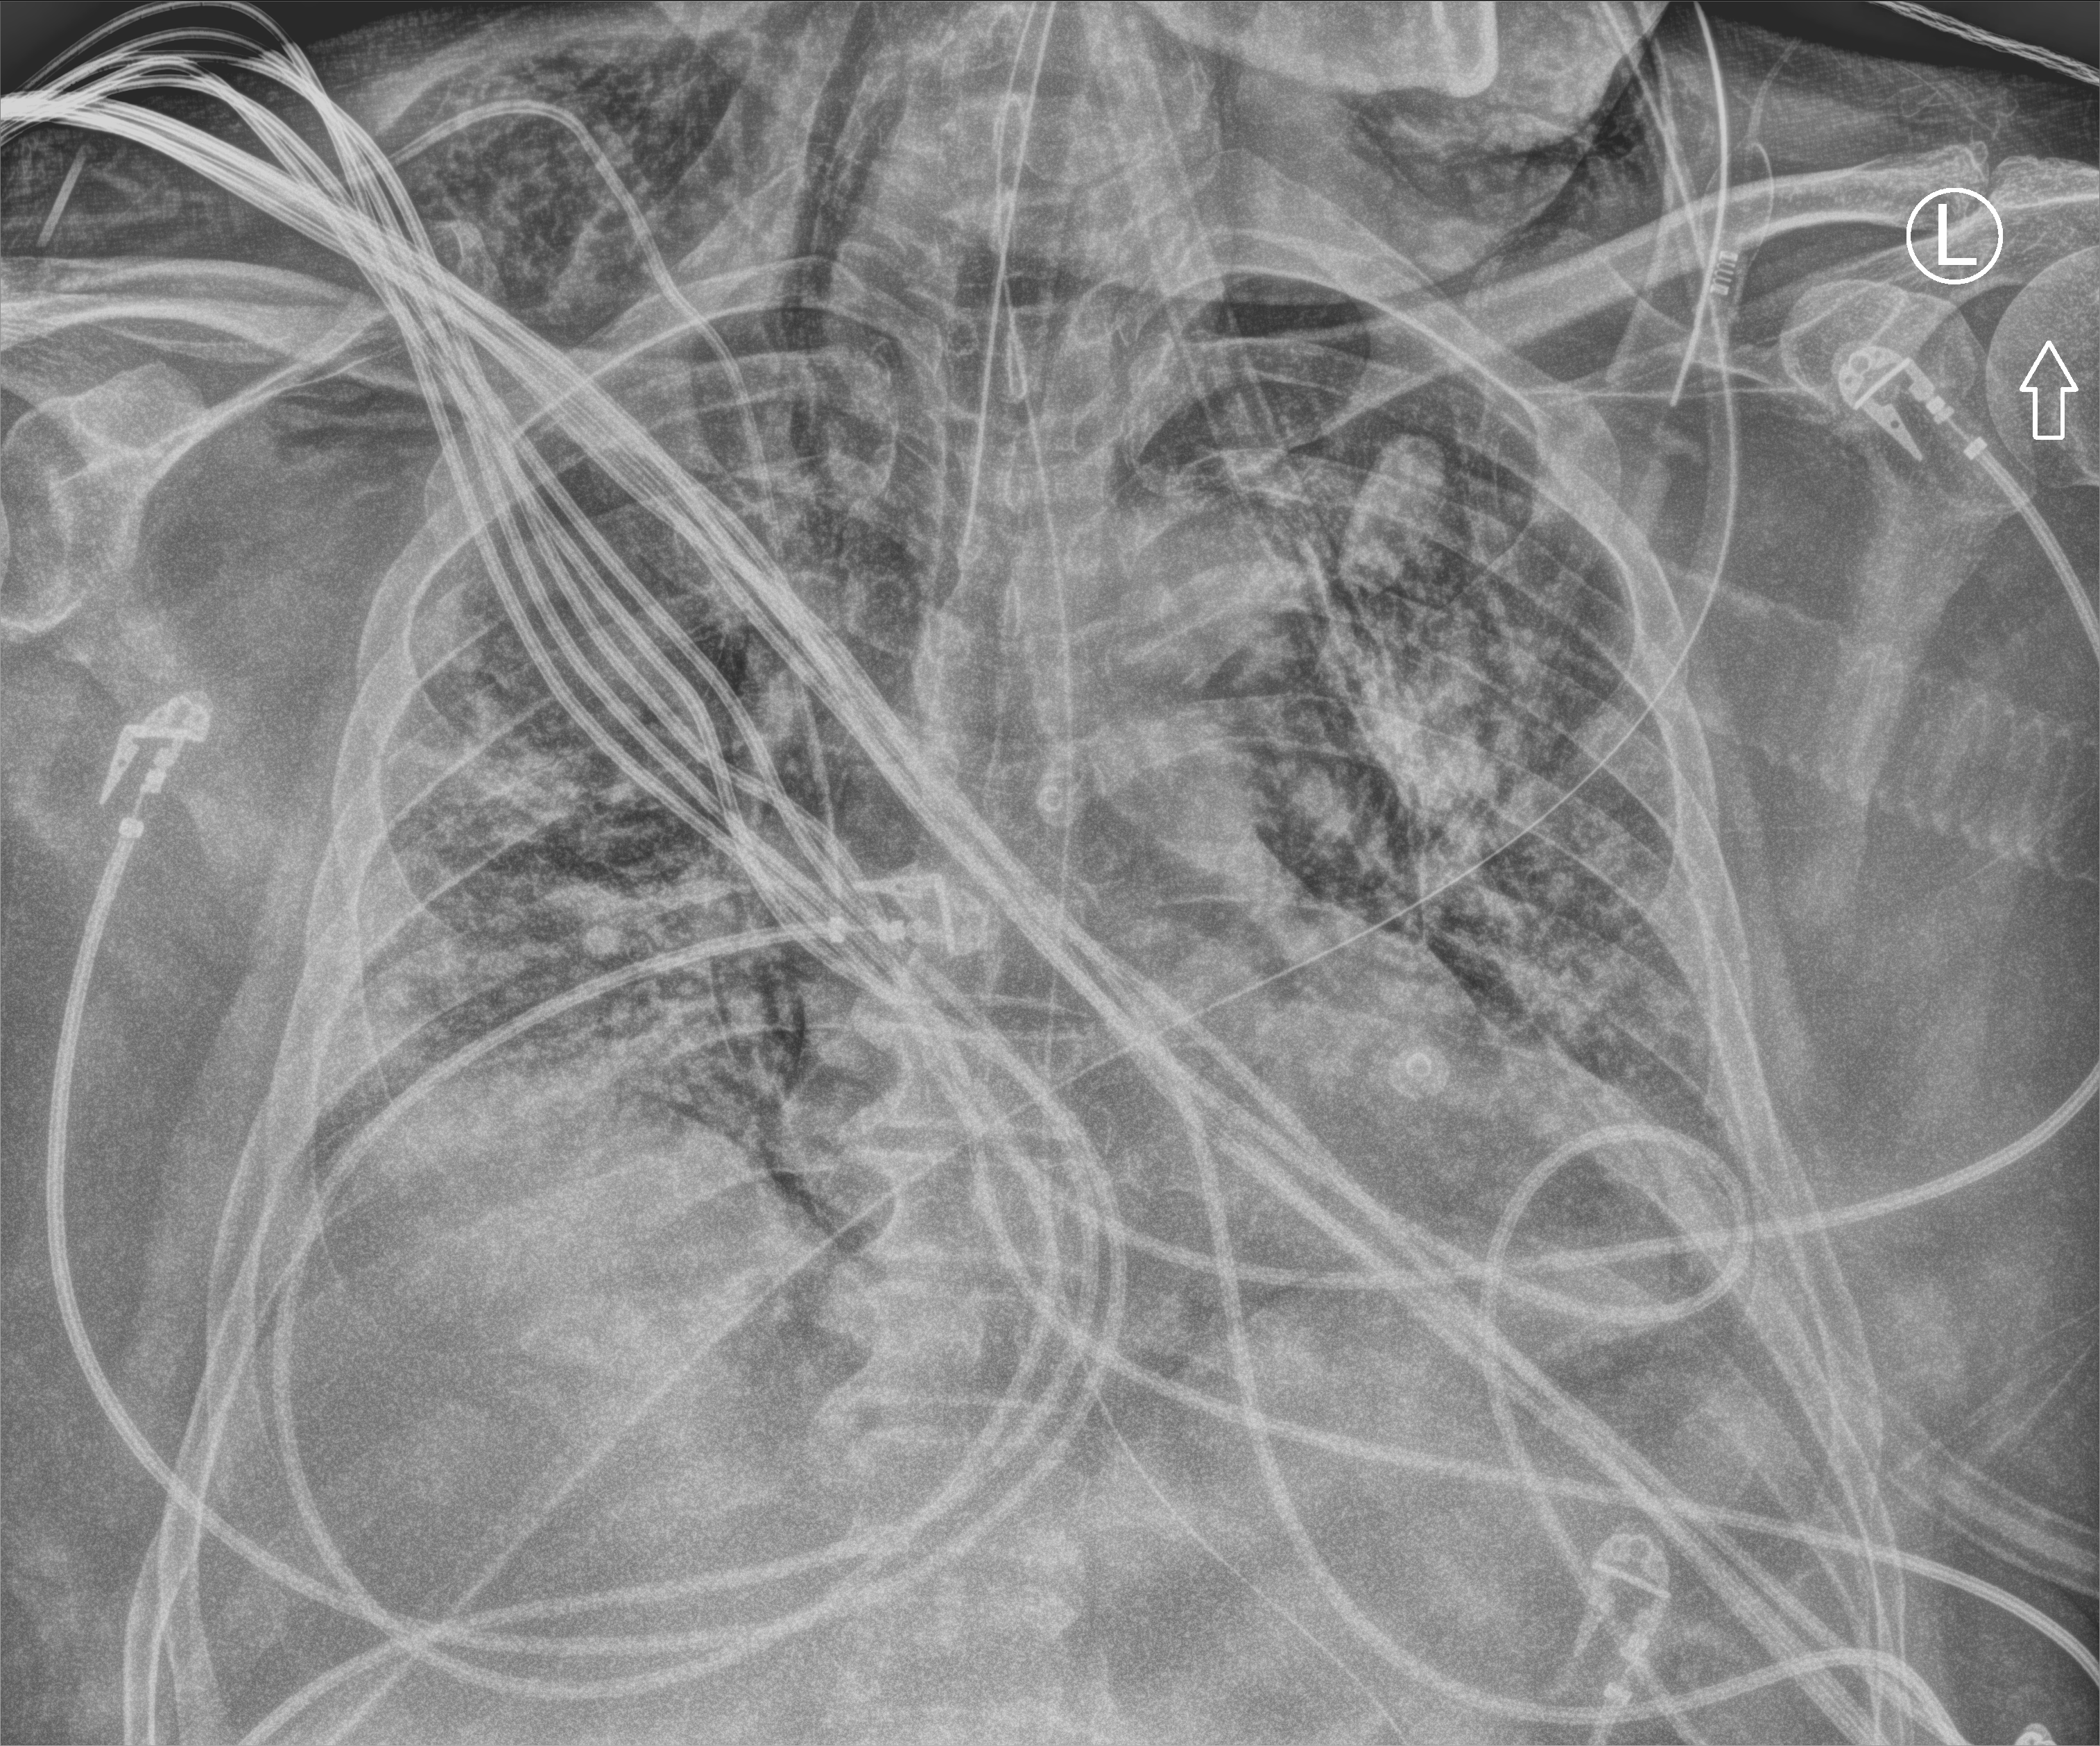
Bedside chest radiograph (computed radiography), anteroposterior (AP) projection. Adult patient hospitalised with COVID-19, age 18–59 years.
Admission-level facts for this patient (not findings on this image; timing relative to this image not recorded):
- chronic kidney disease (admission record): no
- mechanically ventilated during this hospital stay: yes